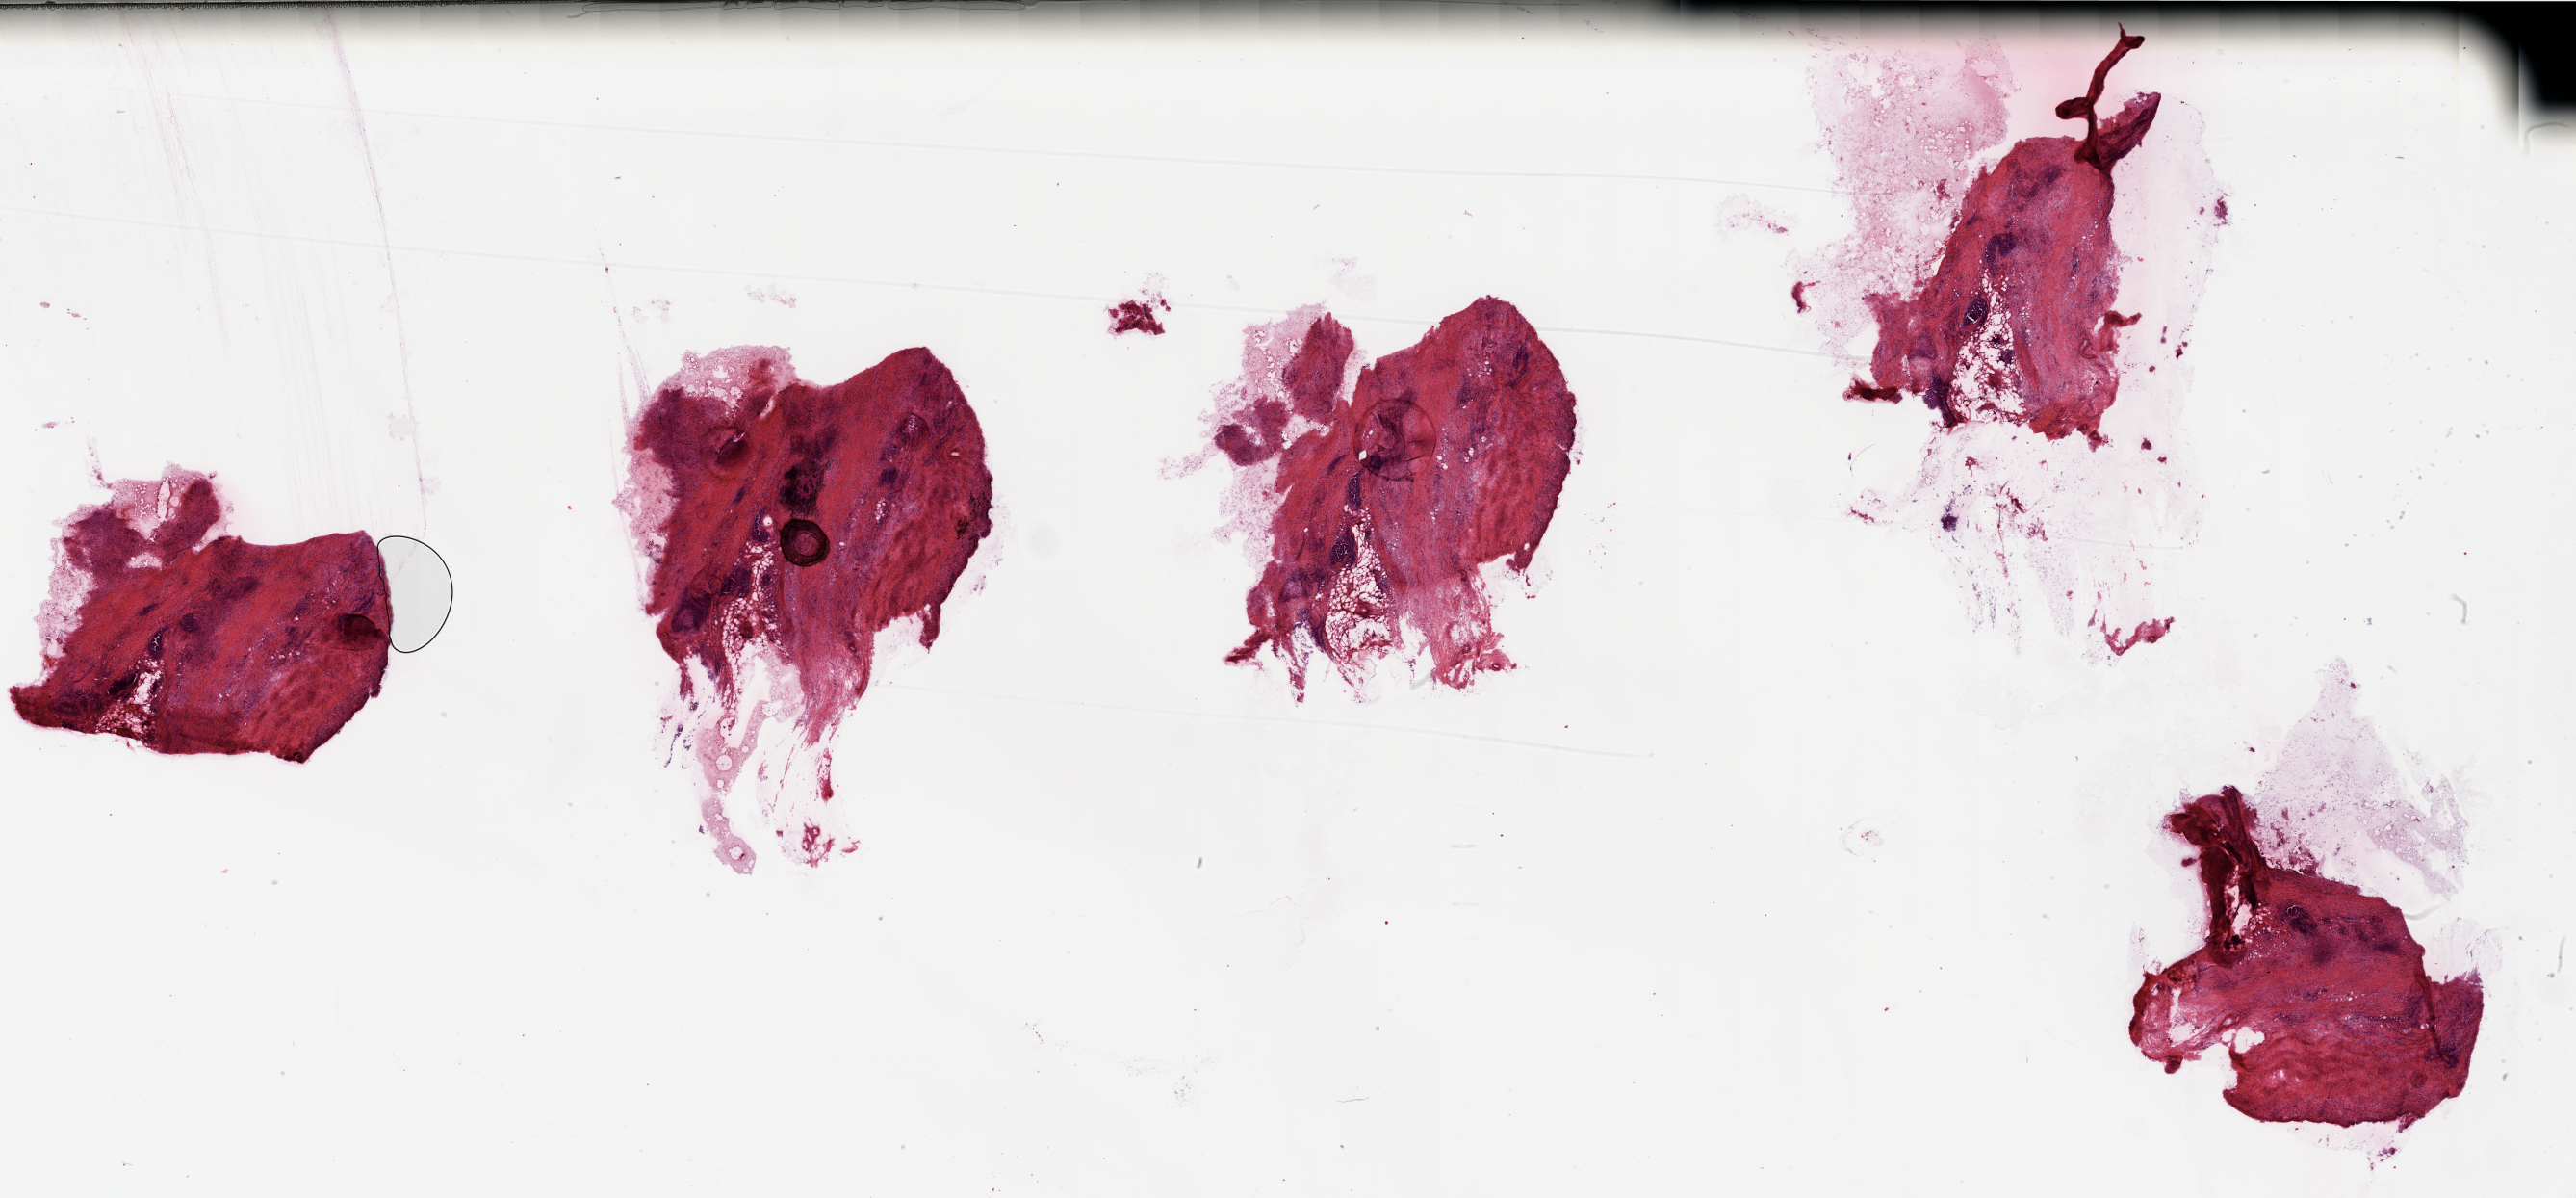
H&E whole-slide image, whole scanned area (about 42.3 x 19.7 mm, acquisition: 20x scan) shown as a low-resolution overview, tumour tissue sample, pancreas. Male, 65 y/o. Histologic grade: G3 (poorly differentiated).
Diagnosis: Infiltrating duct carcinoma, NOS. AJCC pathologic stage: III. Primary tumour site (as recorded): head.